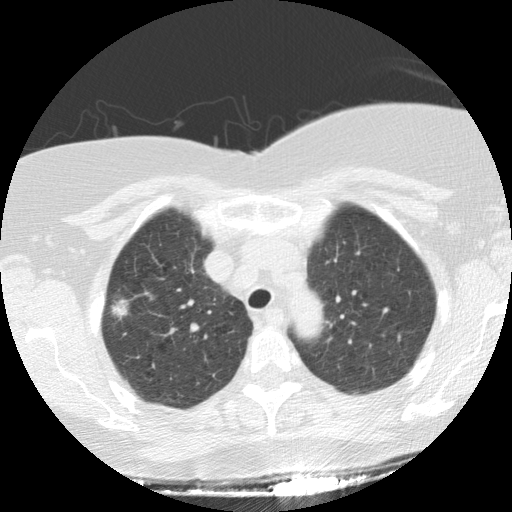
Low-dose screening chest CT, one axial slice. Slice 109 of 136 in the series (ordered by position). Reconstruction kernel STANDARD. Lung window (W 1500 / L -600 HU). 2.5 mm slice thickness. 512 × 512 image matrix, field of view 330 × 330 mm.
Outlined on this slice (manually delineated by an expert):
- lesion 1 (tumor, upper lobe of right lung): bounding box (x1, y1, x2, y2) in pixels: (112, 300, 129, 320)